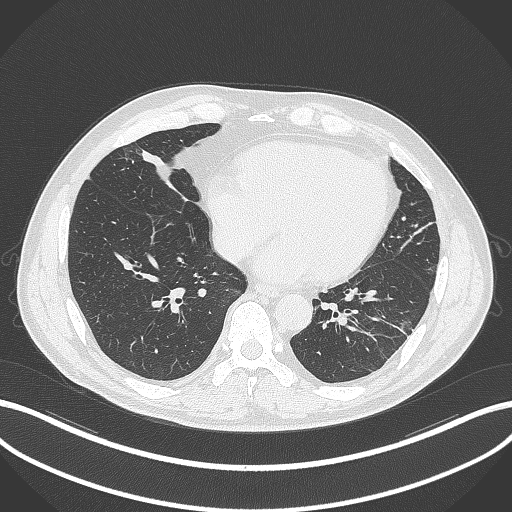
Chest CT, one axial slice. Reconstruction kernel B70f. 120 kVp. Lung window (W 1500 / L -600 HU). 512 × 512 image matrix, field of view 400 × 400 mm. Male patient, age 59 years. From the clinical record (not read from this slice): clinical TNM (as recorded): T2a N1 M0.
Outlined on this slice (bounding box drawn by a radiologist):
- lung tumour (recorded histology: adenocarcinoma): bounding box (x1, y1, x2, y2) in pixels: (137, 144, 171, 180)